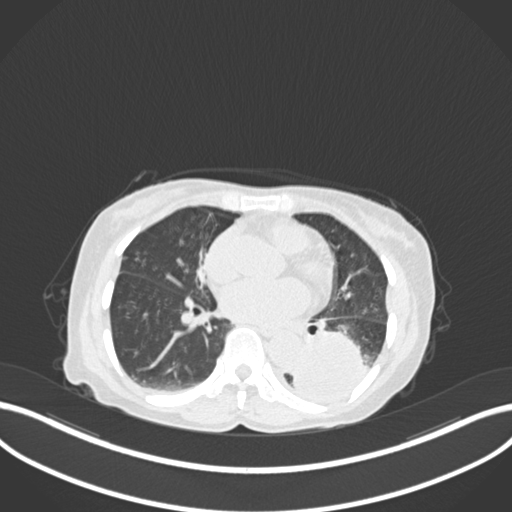
Chest CT, one axial slice; slice 63 of 233 in the series (ordered by position); reconstruction kernel B30f; 120 kVp; lung window (W 1500 / L -600 HU); 512 × 512 image matrix. Patient: female, 78 years. From the clinical record (not read from this slice): clinical TNM (as recorded): T3 N0 M1.
Annotated regions visible in this slice (rectangle marked by the reading radiologist):
- lung tumour (recorded histology: squamous cell carcinoma): bounding box [x1, y1, x2, y2] px = [291, 328, 370, 409]